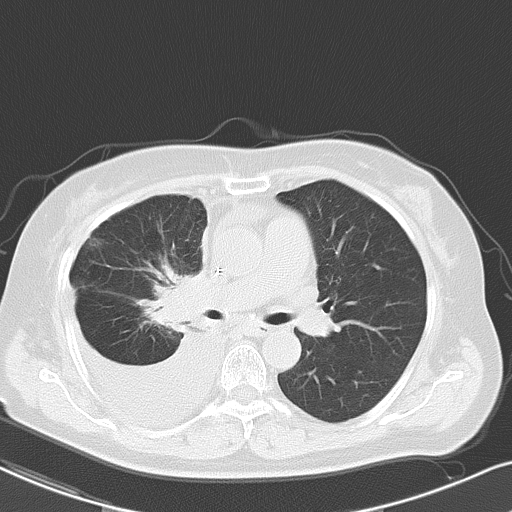
Chest CT, one axial slice; position 30 of 48 along the scan axis; 120 kVp; lung window (W 1500 / L -600 HU); 5 mm slice thickness; 512 × 512 image matrix. Patient: female, 69 years. Case-level facts recorded for this patient, not image findings: clinical TNM (as recorded): T2a N0 M1c.
Structures marked on this image (rectangle marked by the reading radiologist):
- lung tumour (recorded histology: adenocarcinoma): bounding box (x1, y1, x2, y2) in pixels: (151, 254, 219, 333)